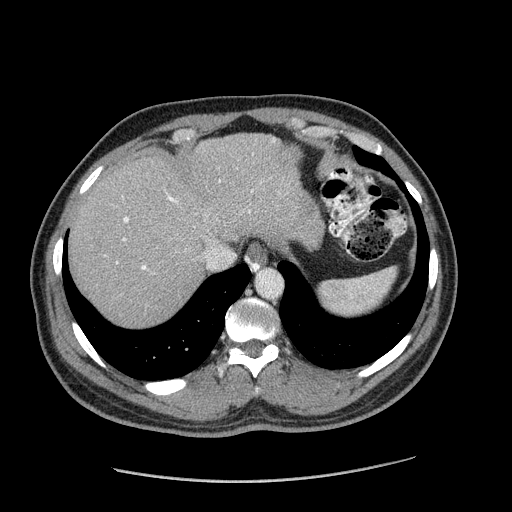
Contrast-enhanced abdominal CT (liver protocol), one axial slice; position 147 of 182 along the scan axis; reconstruction kernel STANDARD; soft-tissue window (W 400 / L 40 HU); 512 × 512 image matrix, field of view 400 × 400 mm. From the clinical record (not read from this slice): diagnosis: hepatocellular carcinoma (patient treated with transarterial chemoembolisation; whether this scan precedes or follows treatment is not stated here); TNM stage (as recorded): Stage-I; Child-Pugh class: A; tumour differentiation: well differentiated; tumour nodularity: uninodular.
Annotated regions visible in this slice (semi-automatic segmentation, software-assisted and operator-edited):
- abdominal aorta: bounding box (x1, y1, x2, y2) in pixels: (258, 271, 283, 298)
- liver parenchyma outside the tumour (the mass and vessels are separate outlines, so this box may not span the whole liver): (68, 134, 324, 326)
- liver vessels: (105, 140, 275, 270)